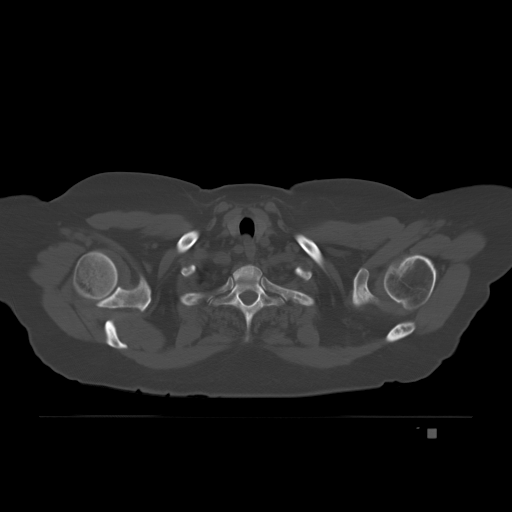
CT including the spine, one axial slice. Slice 174 of 221 in the series (ordered by position). Bone window (W 1800 / L 400 HU). 3 mm slice thickness. 512 × 512 image matrix, field of view 474 × 474 mm. Female patient, age 63 years. Case-level facts recorded for this patient, not image findings: primary cancer: breast.
Outlined on this slice (semi-automatic segmentation, software-assisted and operator-edited):
- T3 vertebra: box from (x=230, y=278) to (x=234, y=282) px